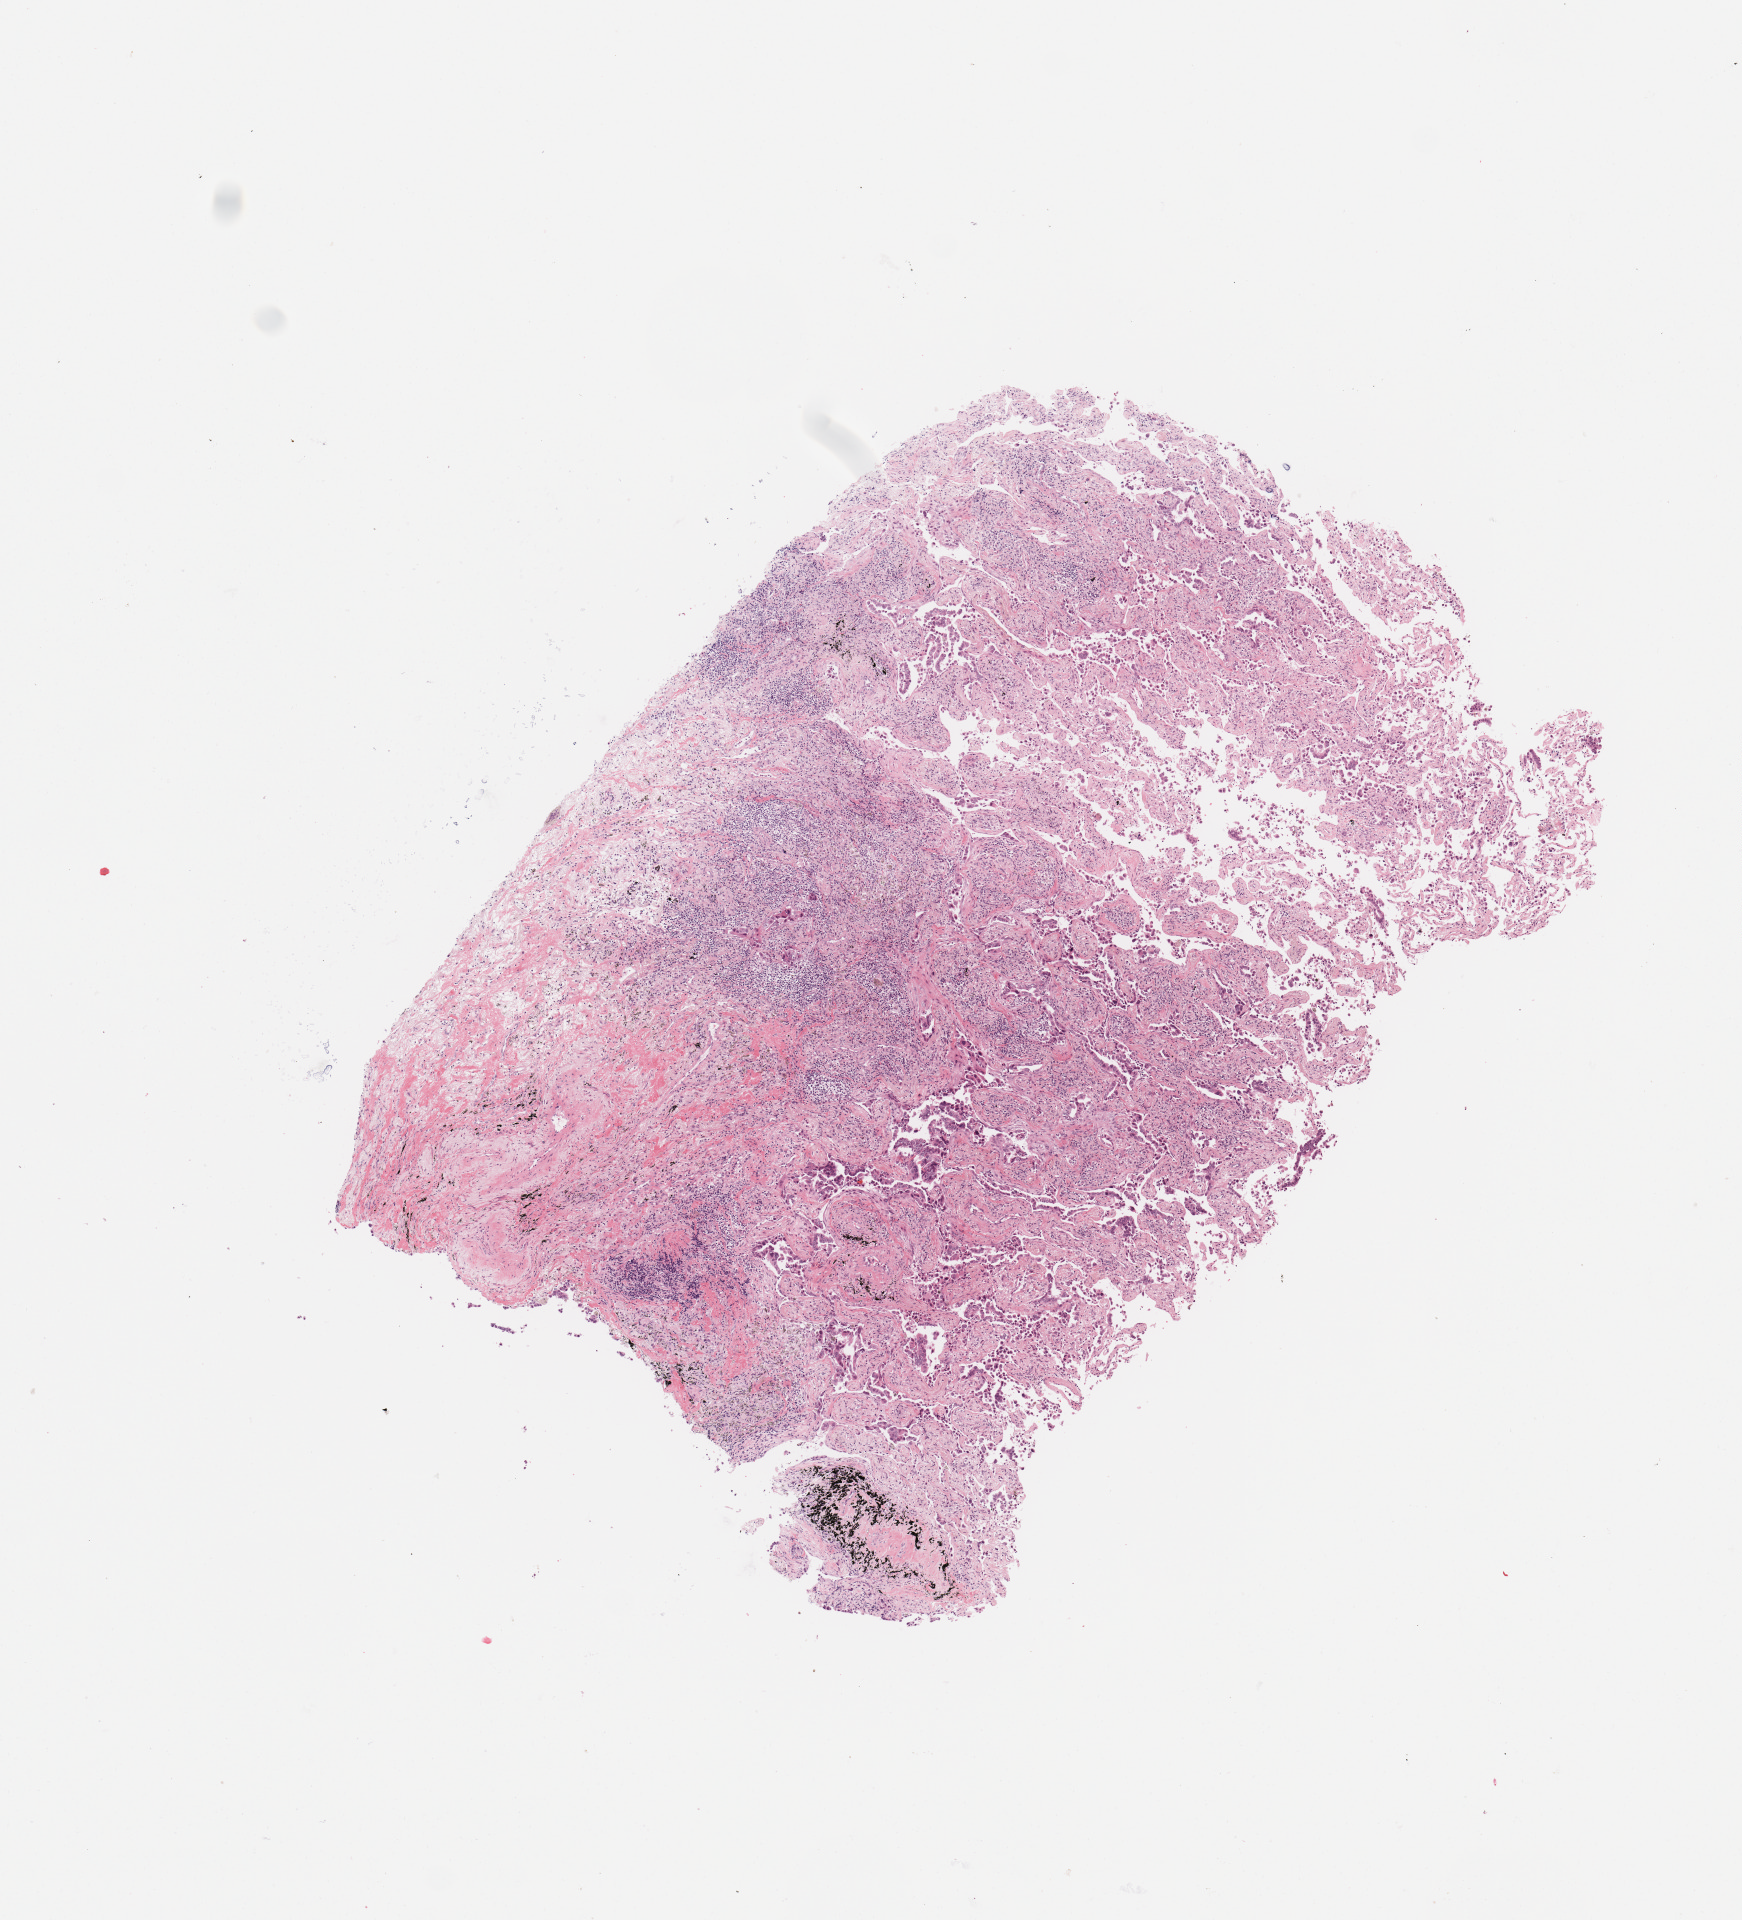
Digitized H&E tissue section (whole slide), whole scanned area (about 6.9 x 7.6 mm, acquisition: 20x scan) shown as a low-resolution overview. Lung, tumour tissue. 72-year-old male patient.
Histologic diagnosis: Adenocarcinoma, NOS.